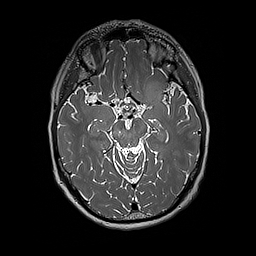
Brain MRI from a brain-tumour surgery series, one axial slice; position 115 of 192 along the scan axis; 256 × 256 image matrix, field of view 250 × 250 mm. From the clinical record (not read from this slice): histopathology: Glioblastoma; WHO grade: 4; IDH mutation: no; tumour location: Left Insular.
Outlined on this slice (manually delineated by an expert):
- tumour: box from (x=140, y=80) to (x=171, y=110) px